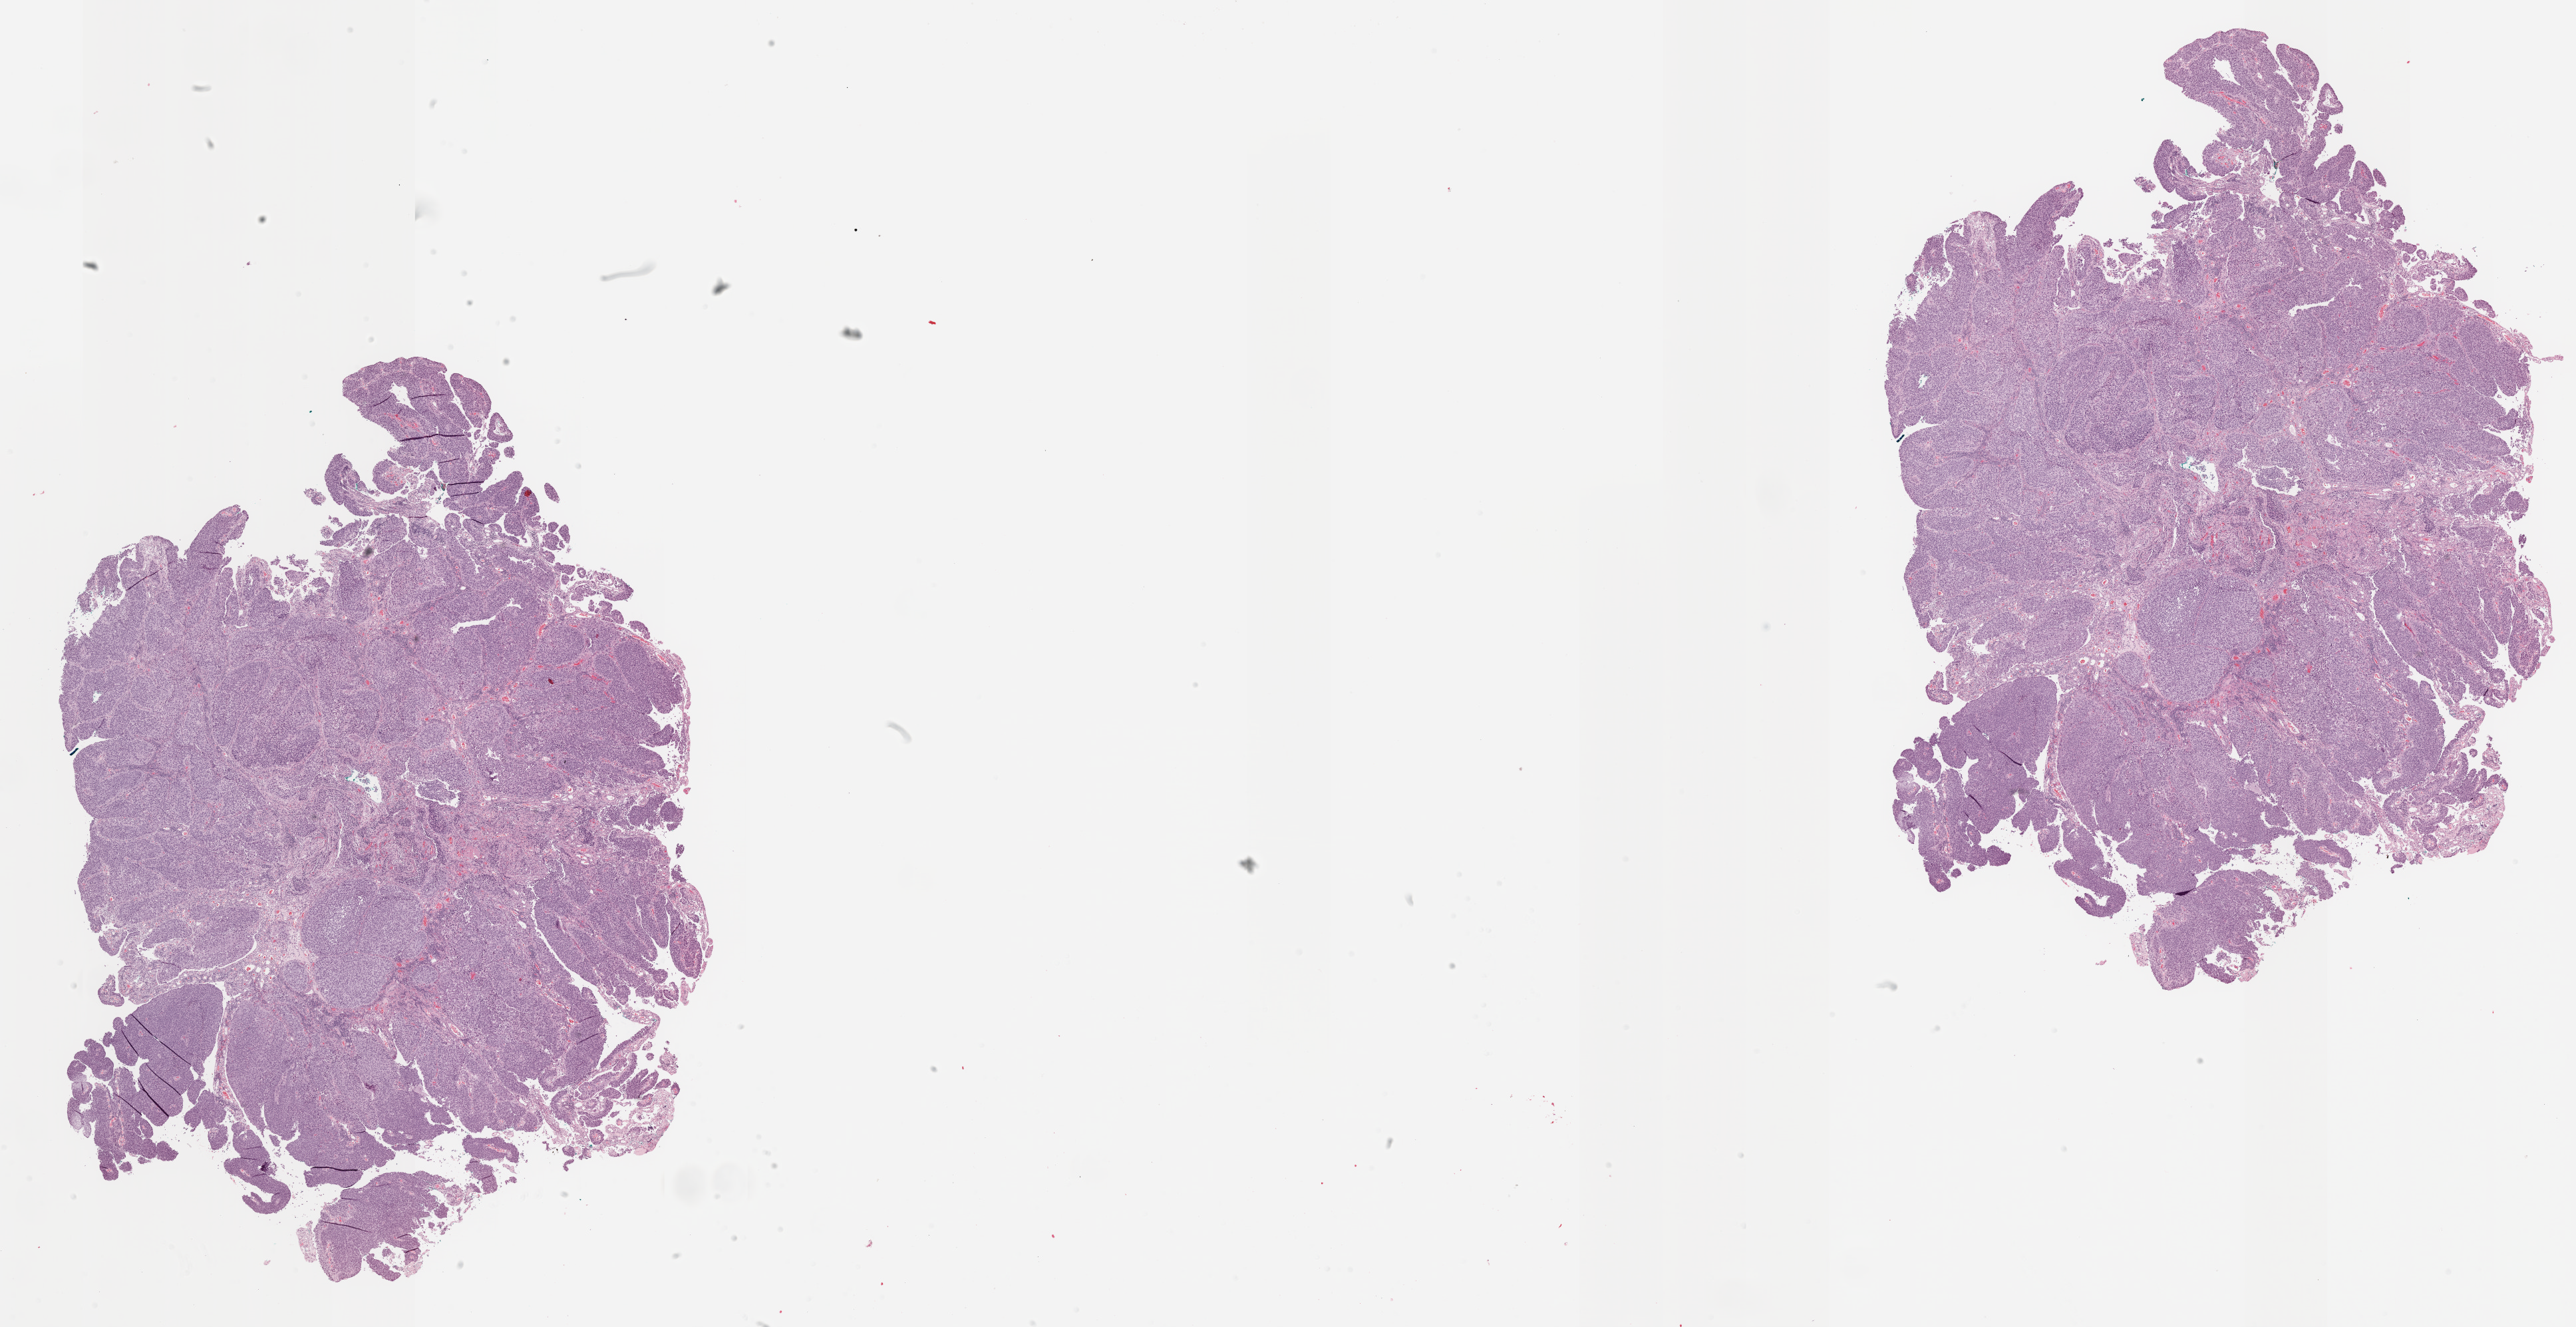
H&E whole-slide image, shown as a low-resolution overview of the whole scanned area (about 31.0 x 16.0 mm, from a 20x scan). Formalin-fixed paraffin-embedded (FFPE) diagnostic section. Primary tumour sample from the bladder. Male patient; age at initial diagnosis 69 years.
Pathologic diagnosis: Transitional cell carcinoma.